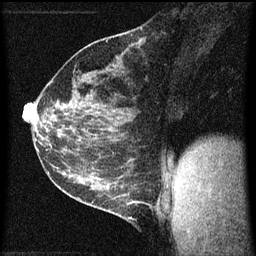
Breast MRI (dynamic contrast-enhanced), one sagittal slice; position 28 of 60 along the scan axis; dynamic contrast-enhanced series, image 2 of 3 at this slice position (ordered by acquisition); 1.5 T; TE 4.2 ms, TR 8 ms; 2 mm slice thickness; 256 × 256 image matrix. Female patient, age 35 years.
Outlined on this slice (semi-automatically segmented with operator editing):
- analysis volume of interest (the breast-tissue region the enhancement analysis was run in; not a lesion): box from (x=106, y=182) to (x=149, y=223) px
- tumour enhancement mask (voxels above the 70 % enhancement threshold inside the analysis volume of interest): (x=114, y=194)–(x=149, y=219)